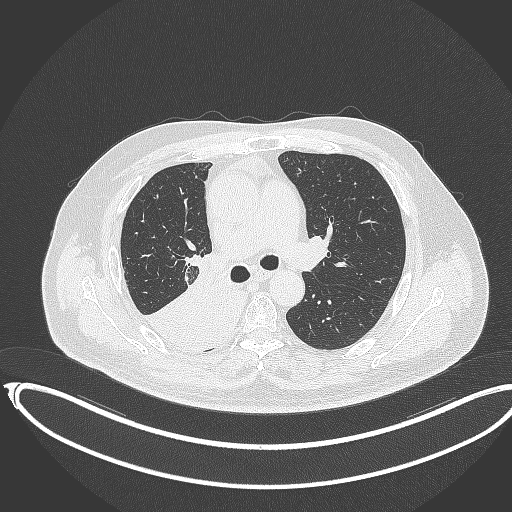
Chest CT, one axial slice; slice 222 of 403 in the series (ordered by position); reconstruction kernel B70f; lung window (W 1500 / L -600 HU); 1 mm slice thickness; 512 × 512 image matrix. Male patient, age 68 years. From the clinical record (not read from this slice): clinical TNM (as recorded): T2a N0 M0.
Annotated regions visible in this slice (rectangle marked by the reading radiologist):
- lung tumour (recorded histology: adenocarcinoma): box from (x=143, y=258) to (x=250, y=347) px